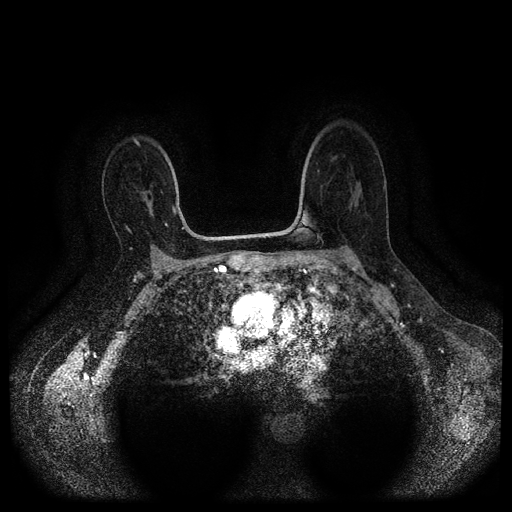
Breast MRI (dynamic contrast-enhanced, multi-phase), one axial slice; position 62 of 112 along the scan axis; dynamic contrast-enhanced series, time point 2 of 5 at this slice position (early post-contrast); 1.5 T; TE 2.6 ms, TR 5.4 ms; 2 mm slice thickness; 512 × 512 image matrix, field of view 340 × 340 mm. Patient: female, 53 years.
Annotated regions visible in this slice (semi-automatically segmented with operator editing):
- breast lesion (labelled 'tumour' in the annotation; benign lesions carry a separate 'benign' label): bounding box (x1, y1, x2, y2) in pixels: (138, 185, 154, 218)